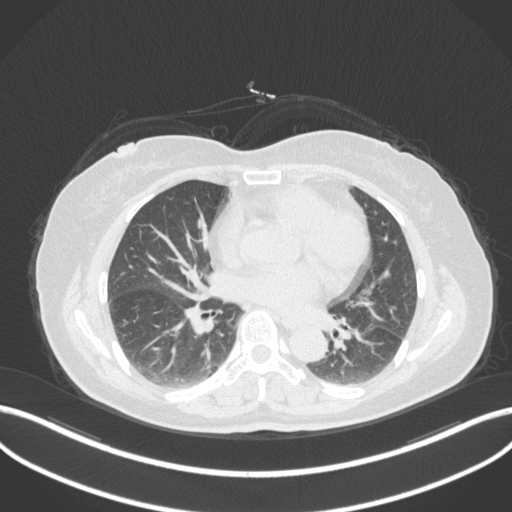
Chest CT, one axial slice. Slice 175 of 307 in the series (ordered by position). Reconstruction kernel B31f. Lung window (W 1500 / L -600 HU). 1 mm slice thickness. 512 × 512 image matrix, field of view 400 × 400 mm. Female patient, age 59 years. Case-level facts recorded for this patient, not image findings: clinical TNM (as recorded): T2a N0 M0; histopathological grade: G2-3.
Structures marked on this image (bounding box drawn by a radiologist):
- lung tumour (recorded histology: adenocarcinoma): bounding box <348,322,384,362> (left, top, right, bottom; pixels)